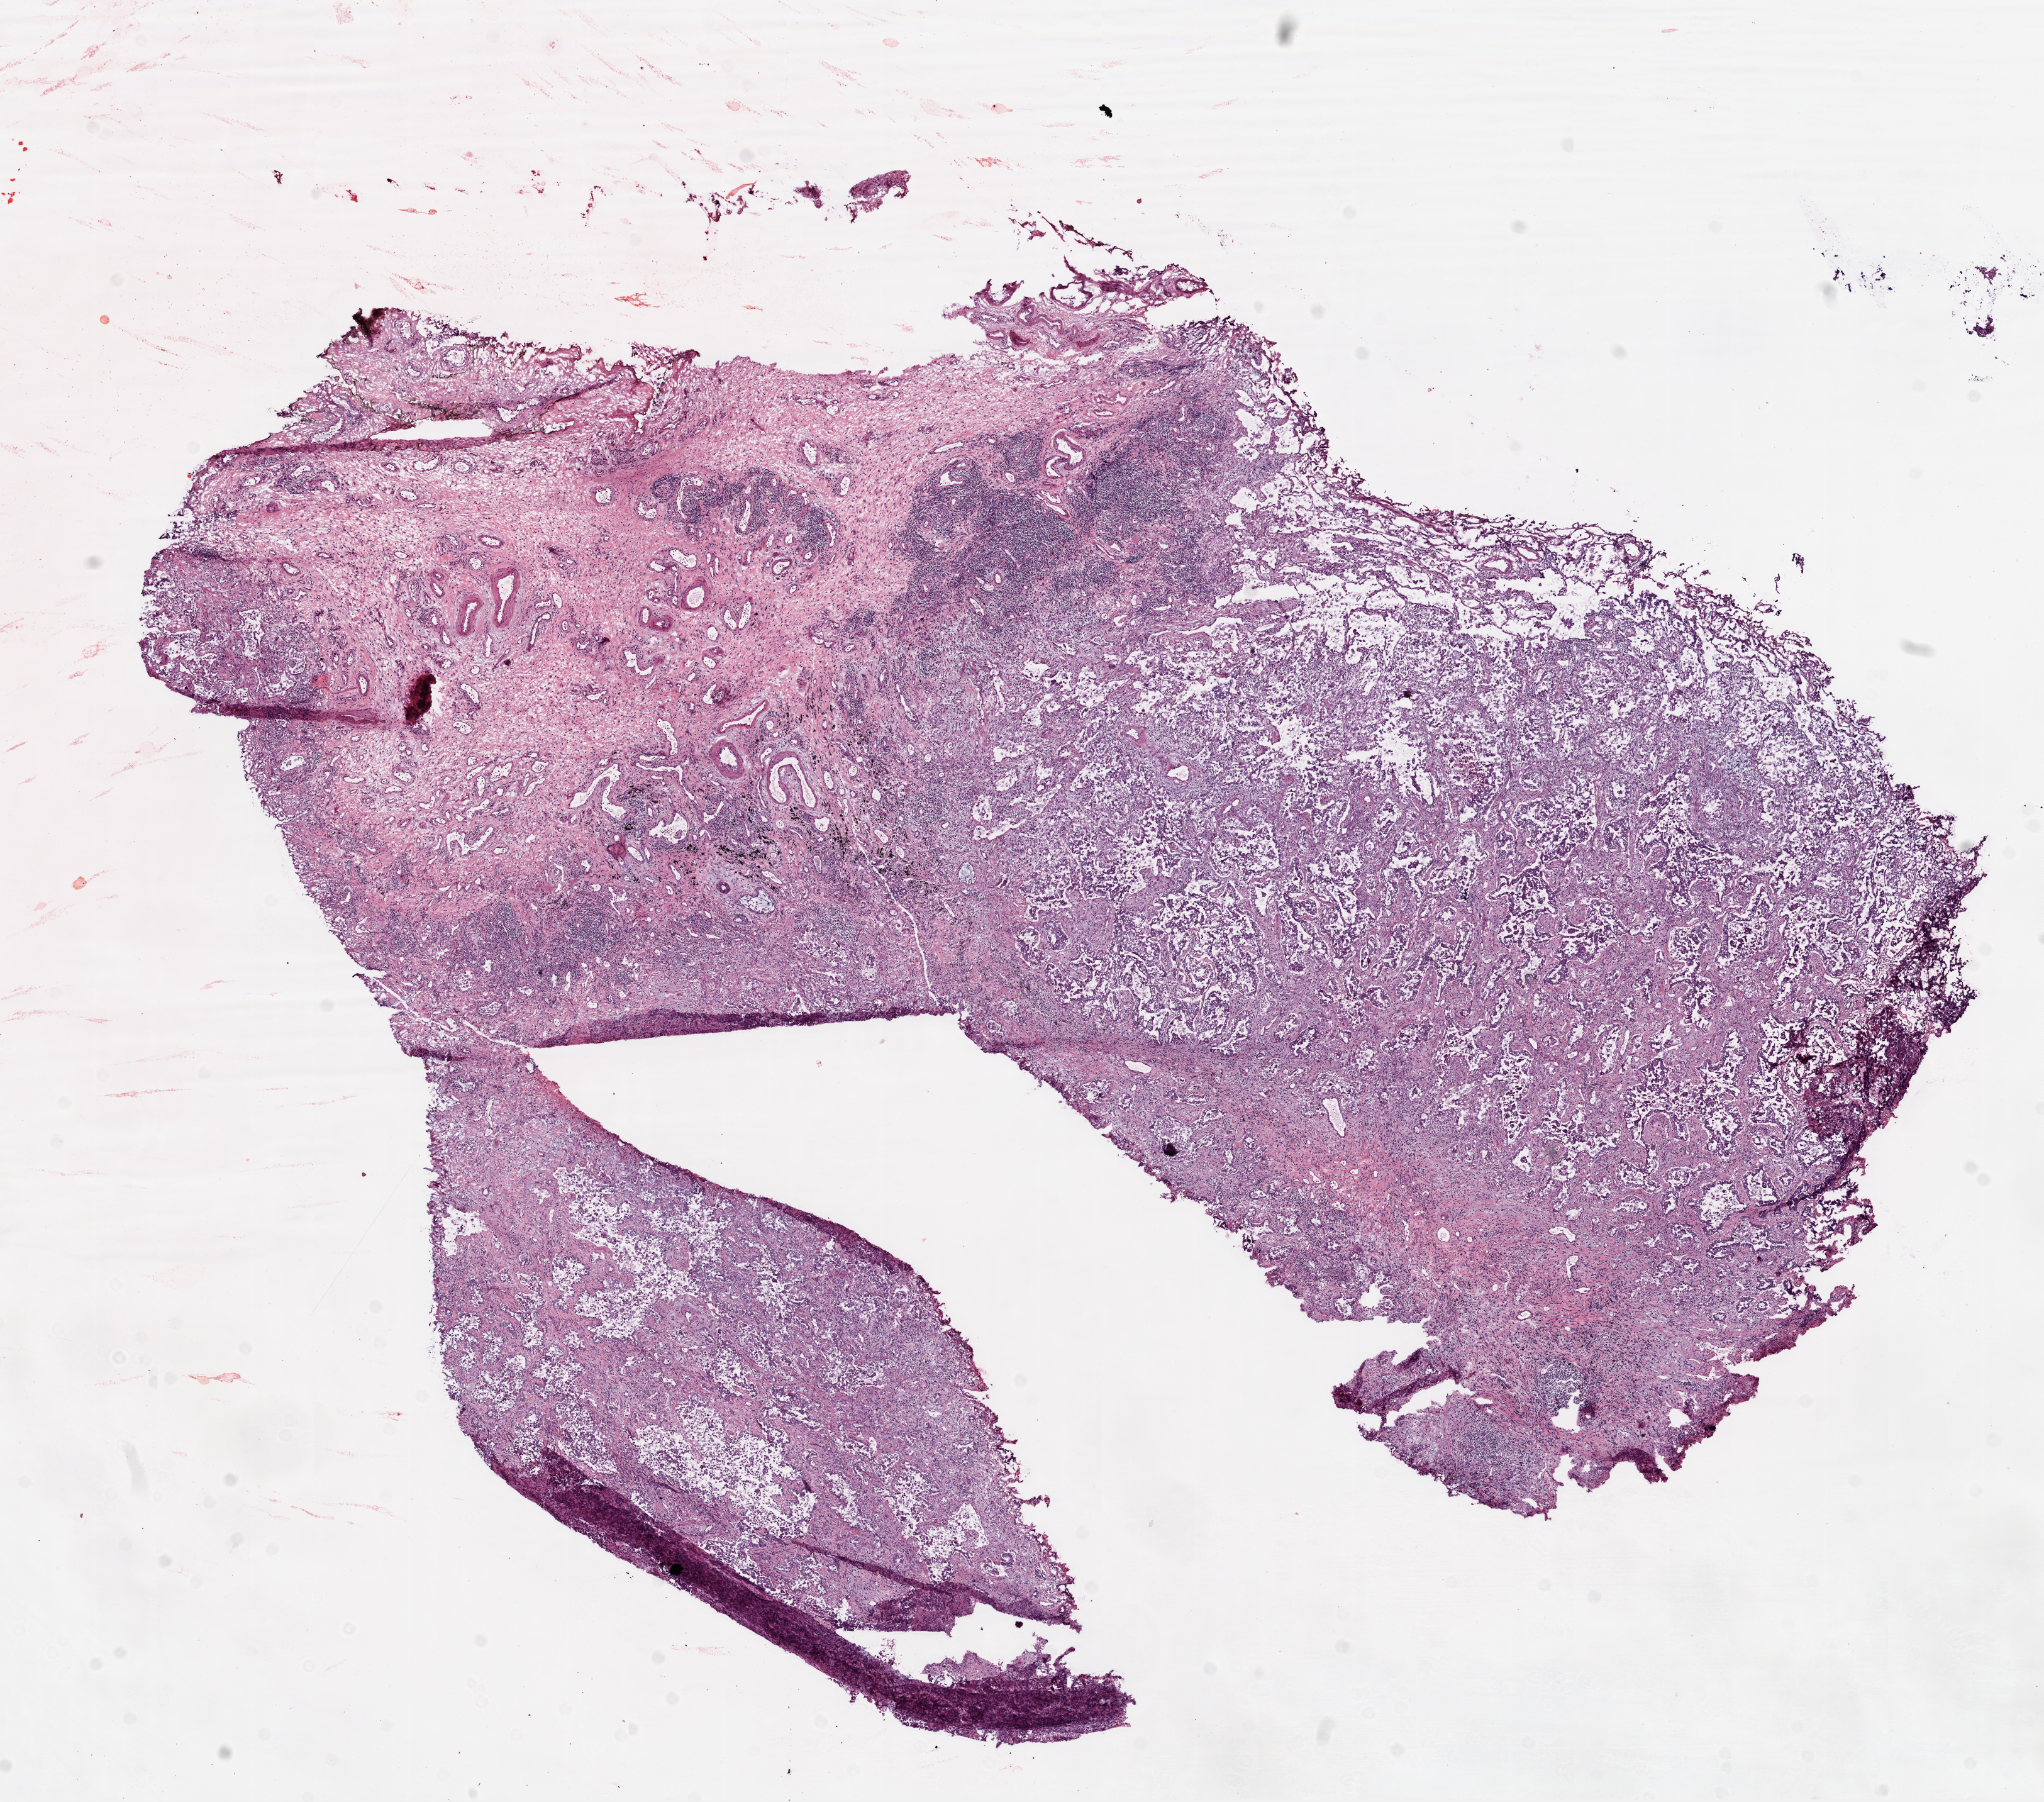
Hematoxylin and eosin (H&E) stained whole-slide image — a low-resolution overview of the entire scanned area, about 13.0 x 11.5 mm (acquisition: 20x scan), frozen section from the top of the tissue portion, primary tumour sample from the lung. Female patient; age at initial diagnosis 80 years. Pathologist review of this section (percent, as recorded): tumour cells 30%, tumour nuclei 40%, normal cells 0%, stromal cells 70%, necrosis 0%.
- TNM: T2 N0 M0
- laterality: left
- AJCC pathologic stage: IB
- histologic diagnosis: Adenocarcinoma, NOS